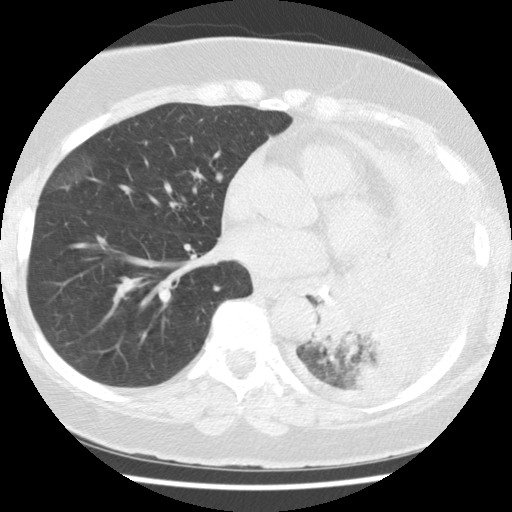
Axial slice from a low-dose chest CT screening exam. Baseline screening round. Lung window (W 1500 / L -600 HU). 2.5 mm slice thickness. Standard (soft-tissue) reconstruction kernel (STANDARD). Female, age 65 years at enrolment. Current smoker at enrolment.
Expert reader's lesion annotation, bounding box <309,282,423,377> (left, top, right, bottom; pixels). Screening reader's record for this exam (one nodule recorded; not confirmed to be the boxed lesion): non-calcified nodule or mass ≥4 mm, left lower lobe, 74 × 48 mm, spiculated (stellate) margins, soft tissue attenuation. Official screen result: positive, change unspecified: nodule(s) >= 4 mm or enlarging nodule(s), mass(es), or other non-specific abnormalities suspicious for lung cancer.